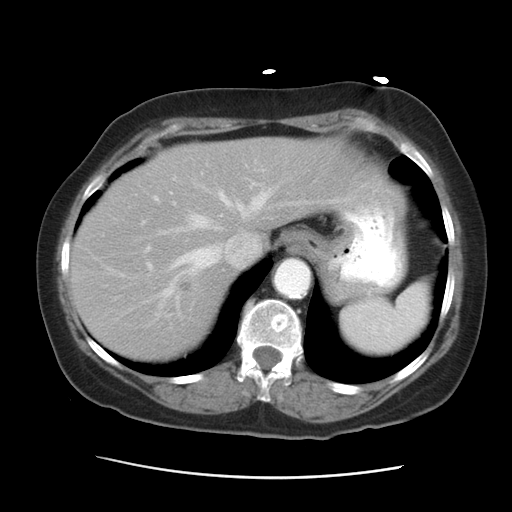
Contrast-enhanced abdominal CT, one axial slice. Slice 23 of 29 in the series (ordered by position). Intravenous contrast given. Soft-tissue window (W 400 / L 40 HU). 7.5 mm slice thickness. 512 × 512 image matrix. Female patient, age 64 years. From the clinical record (not read from this slice): diagnosis: colorectal cancer liver metastases, imaged before liver resection; multiple liver metastases: no; largest metastasis: 2.5 cm; chemotherapy before resection: no.
Outlined on this slice (manually delineated by an expert):
- hepatic veins: bounding box [x1, y1, x2, y2] px = [152, 169, 305, 315]
- liver: [71, 138, 369, 360]
- planned liver remnant (the part of the liver to remain after resection): [71, 139, 369, 273]
- portal vein (with intrahepatic branches): [142, 222, 150, 251]
- liver metastasis: [177, 278, 197, 295]